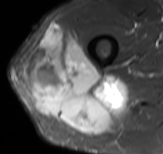
MRI of an extremity soft-tissue mass, one axial slice. Position 49 of 61 along the scan axis. STIR. MR volume resampled by the dataset authors to the PET/CT grid (not the native acquisition matrix). 3.27 mm slice thickness. 163 × 154 image matrix. Male patient. From the clinical record (not read from this slice): histological type: poorly differentiated synovial sarcoma; grade: high; site of the primary tumour: right buttock.
Structures marked on this image (expert contour drawn on MRI and transferred to this co-registered scan by the dataset authors):
- gross tumour volume including surrounding oedema: bounding box [x1, y1, x2, y2] px = [25, 23, 124, 134]
- gross tumour volume (mass): [25, 23, 124, 134]